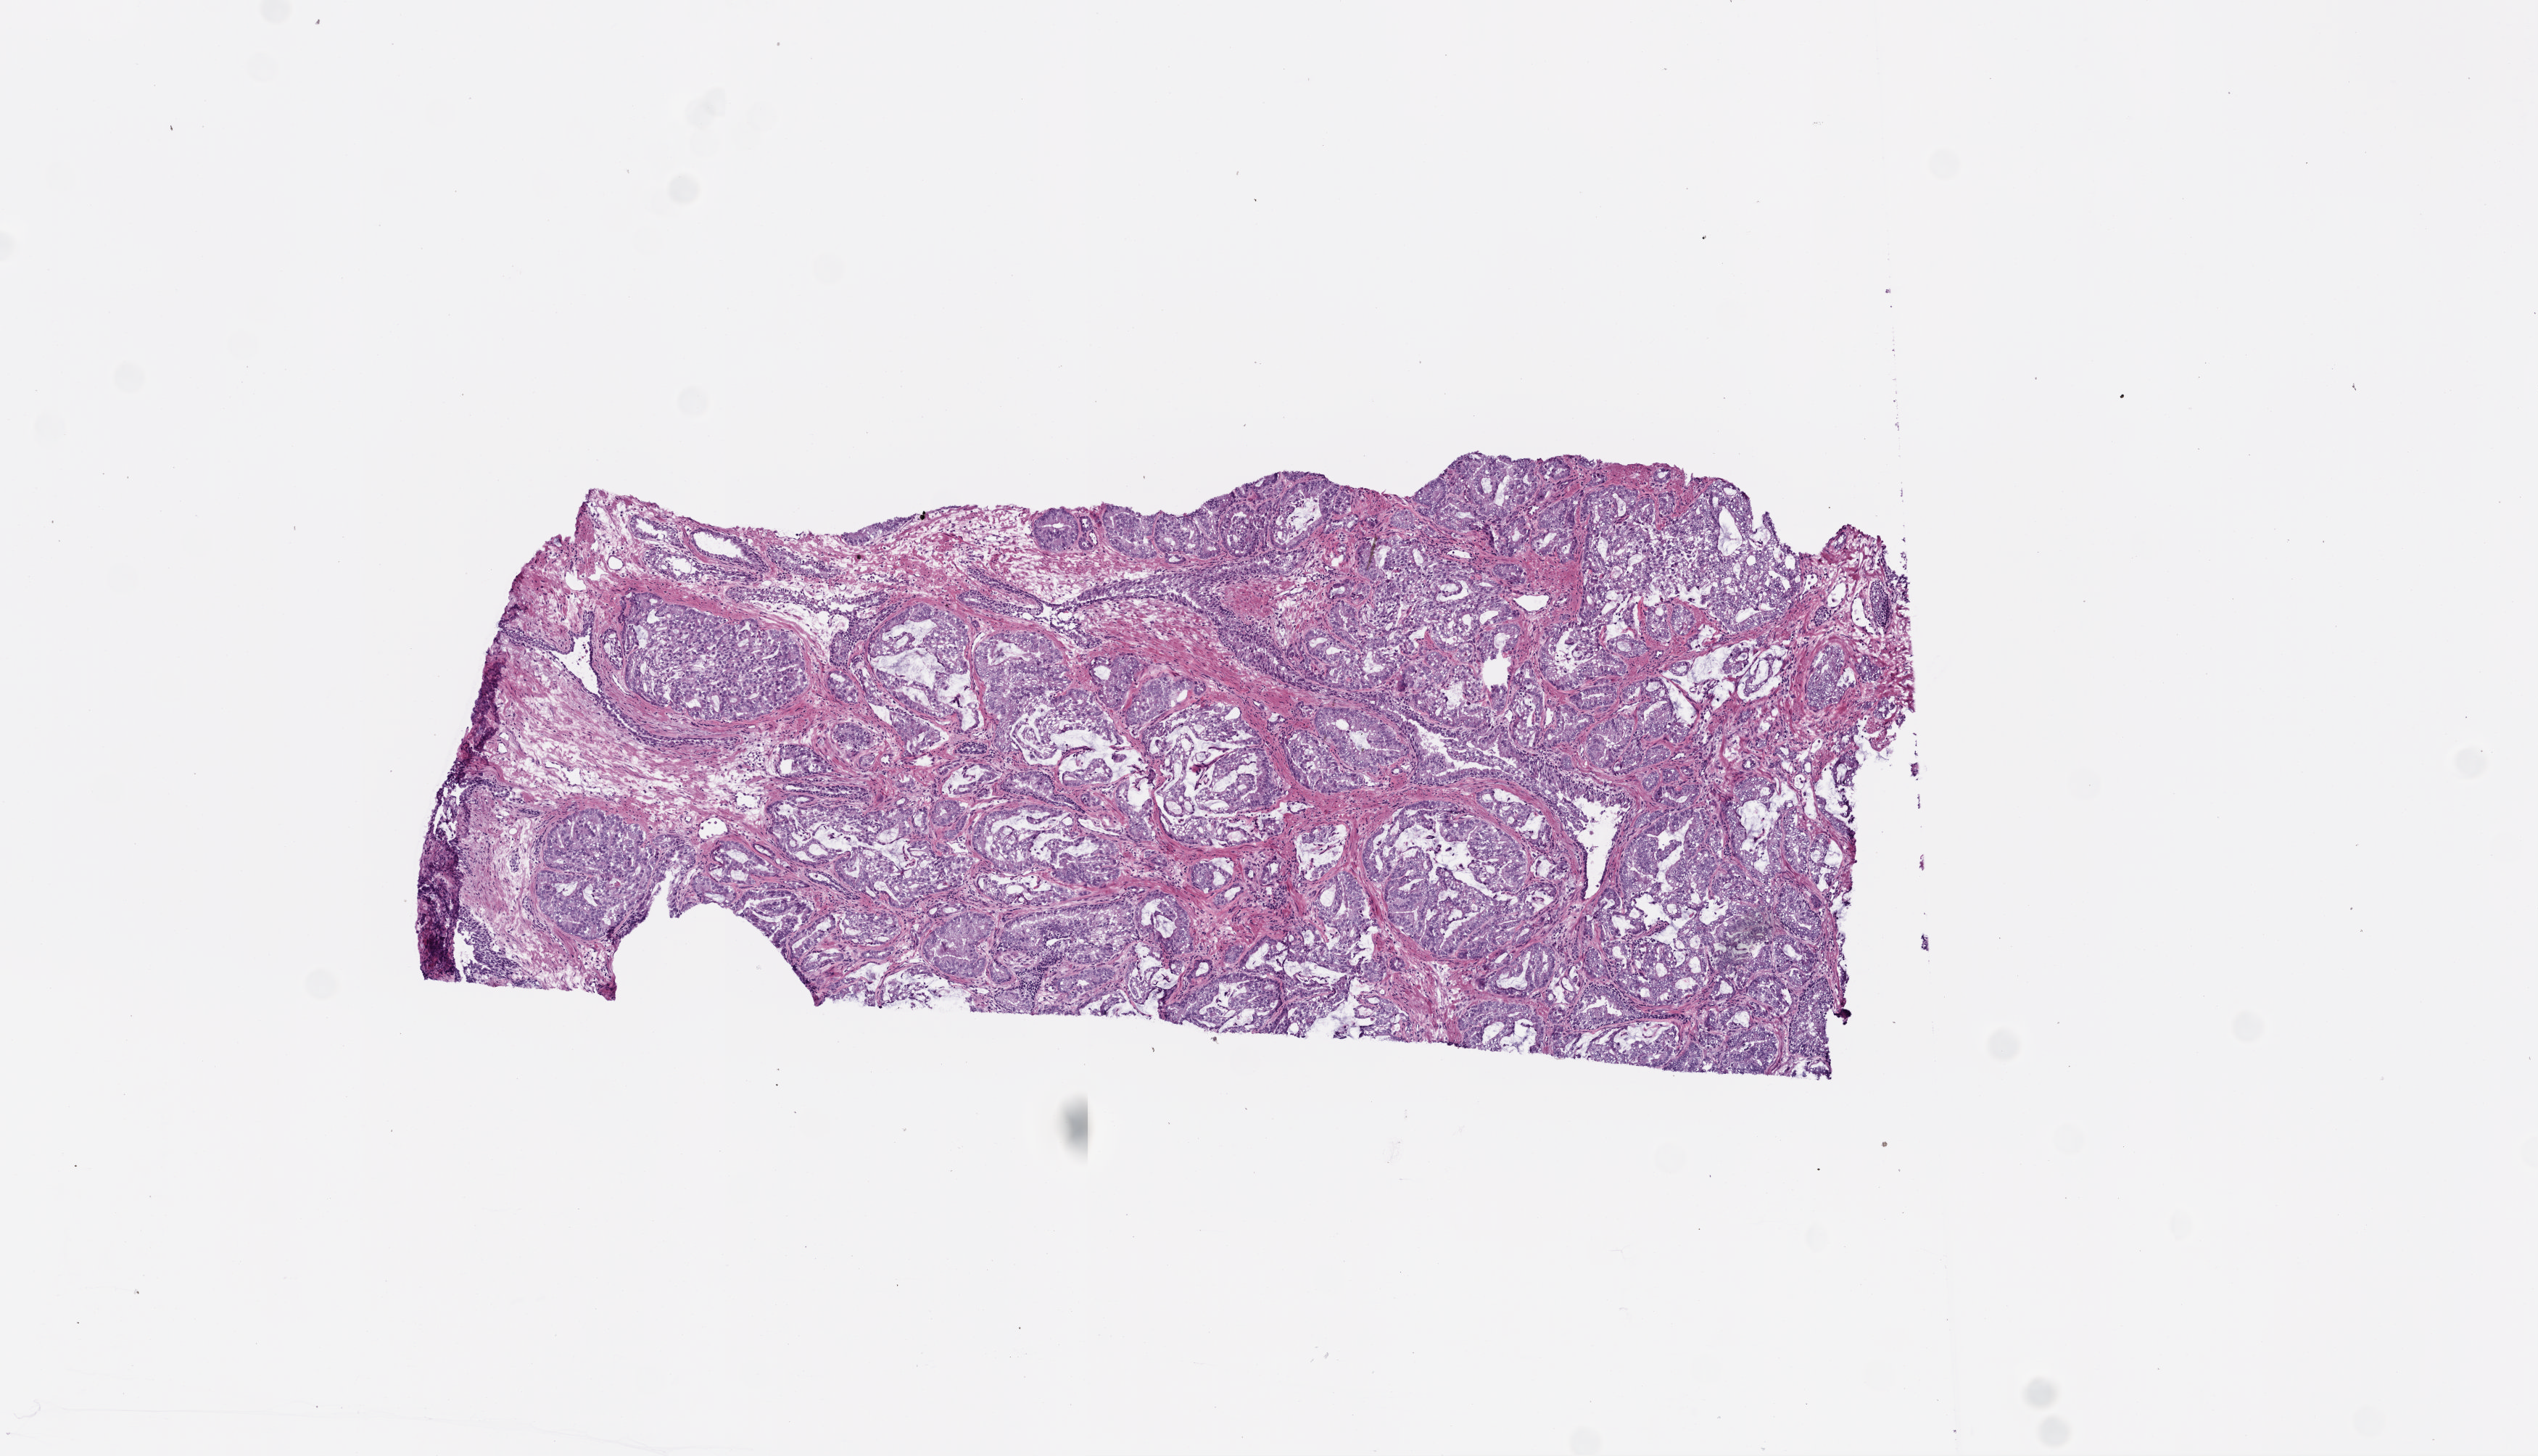
Digitized H&E tissue section (whole slide), a low-resolution overview of the entire scanned area, about 7.0 x 4.0 mm. Frozen section from the bottom of the tissue portion. Sample: primary tumour, prostate. Patient: male, age at initial diagnosis 64 years.
Pathologic diagnosis: Acinar cell carcinoma (prostate gland).